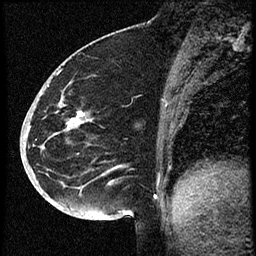
Breast MRI (dynamic contrast-enhanced), one sagittal slice; slice 26 of 60 in the series (ordered by position); dynamic contrast-enhanced study with each time point stored as its own series, time point 2 of 3 at this slice position (early post-contrast, ordered by acquisition time); 1.5 T; TE 4.2 ms, TR 18.9 ms; 2 mm slice thickness; 256 × 256 image matrix. Female patient. From the clinical record (not read from this slice): setting: breast cancer imaged before/during neoadjuvant chemotherapy; receptor status: HR-positive, HER2-negative.
Outlined on this slice (semi-automatic segmentation, software-assisted and operator-edited):
- analysis volume of interest (the breast-tissue region the enhancement analysis was run in; not a lesion): bounding box [x1, y1, x2, y2] px = [30, 87, 114, 173]
- tumour enhancement mask (voxels above the 100 % enhancement threshold inside the analysis volume of interest): [68, 113, 85, 127]